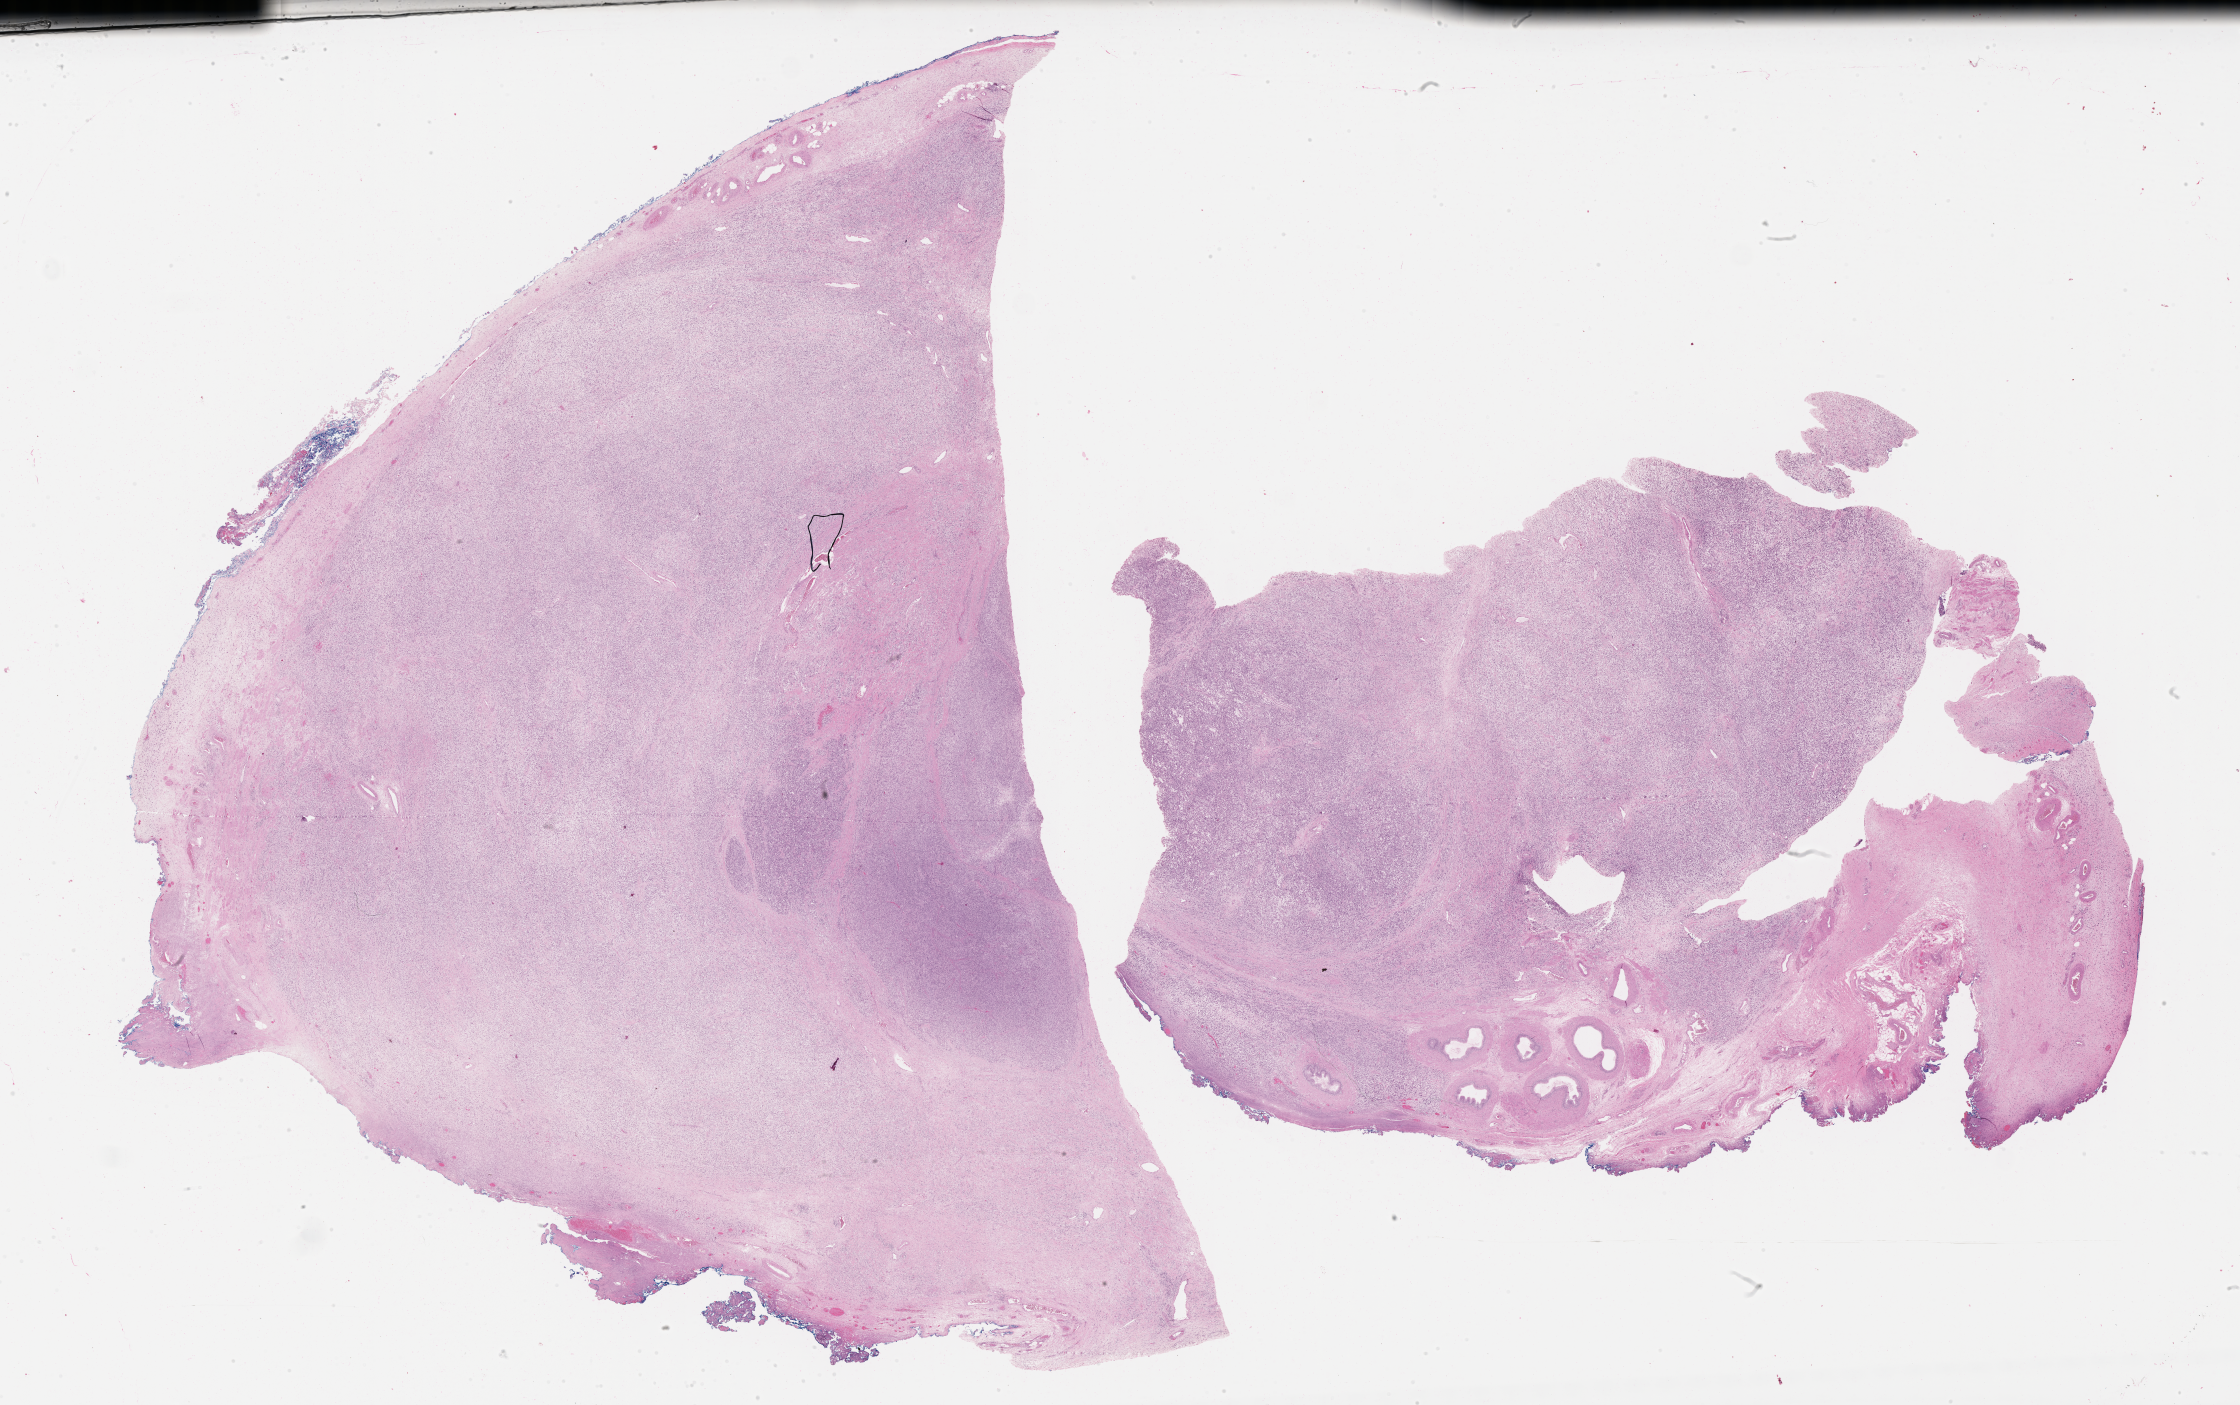
H&E whole-slide image of tumor tissue, low-resolution overview of the scanned area, about 36.2 x 22.7 mm; FFPE section; site: epididymis, right. Male patient, age at diagnosis 24.4 years.
Metastatic status at presentation (as recorded): non-metastatic (confirmed). Stage (as recorded): 2. Diagnosis: rhabdomyosarcoma; histological classification: embryonal rhabdomyosarcoma.